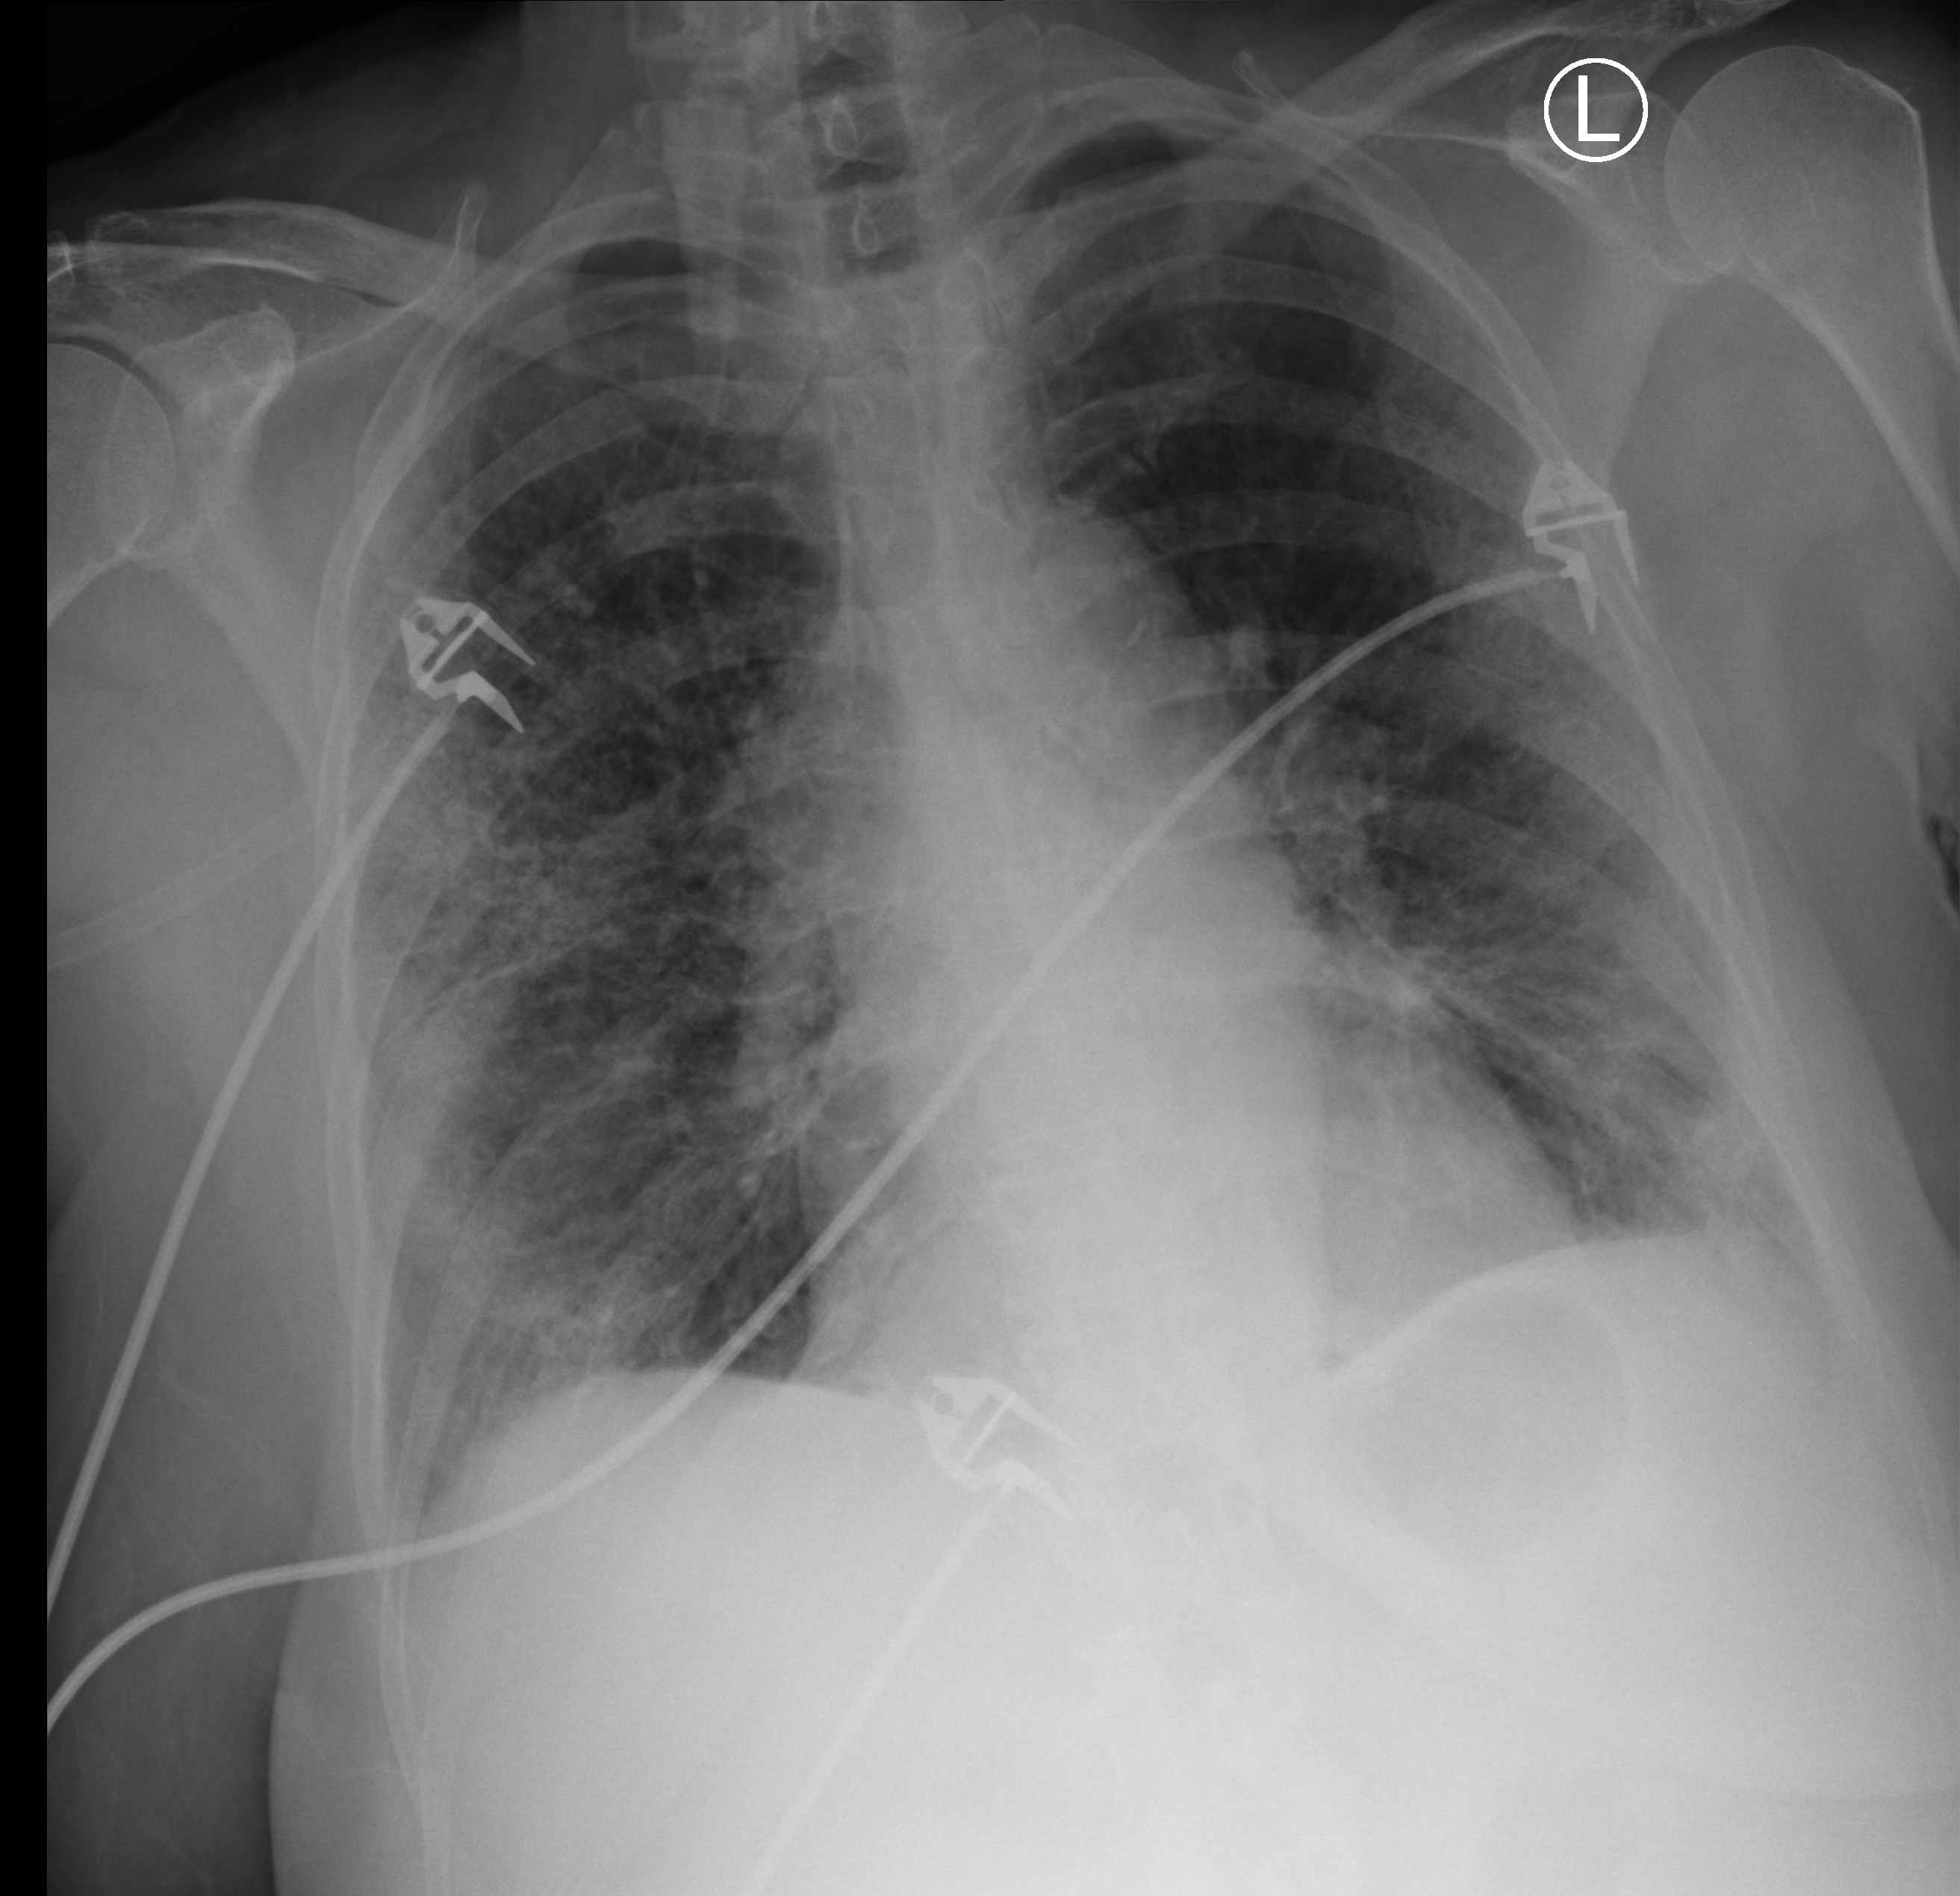
Chest X-ray (portable); anteroposterior (AP) projection. Patient hospitalised with COVID-19; female, aged 60–74 years.
Admission-level facts for this patient (not findings on this image; timing relative to this image not recorded):
- admitted to intensive care during this hospital stay: yes